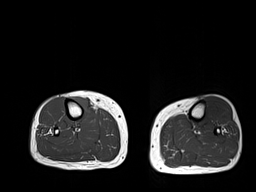
MRI of an extremity soft-tissue mass, one axial slice; position 14 of 32 along the scan axis; 6 mm slice thickness; 256 × 192 image matrix, field of view 375 × 281 mm. Female patient. Case-level facts recorded for this patient, not image findings: histological type: undifferentiated – high grade; grade: high; site of the primary tumour: right thigh.
Structures marked on this image (outlined manually by an expert reader):
- gross tumour volume (mass): box from (x=71, y=94) to (x=95, y=116) px